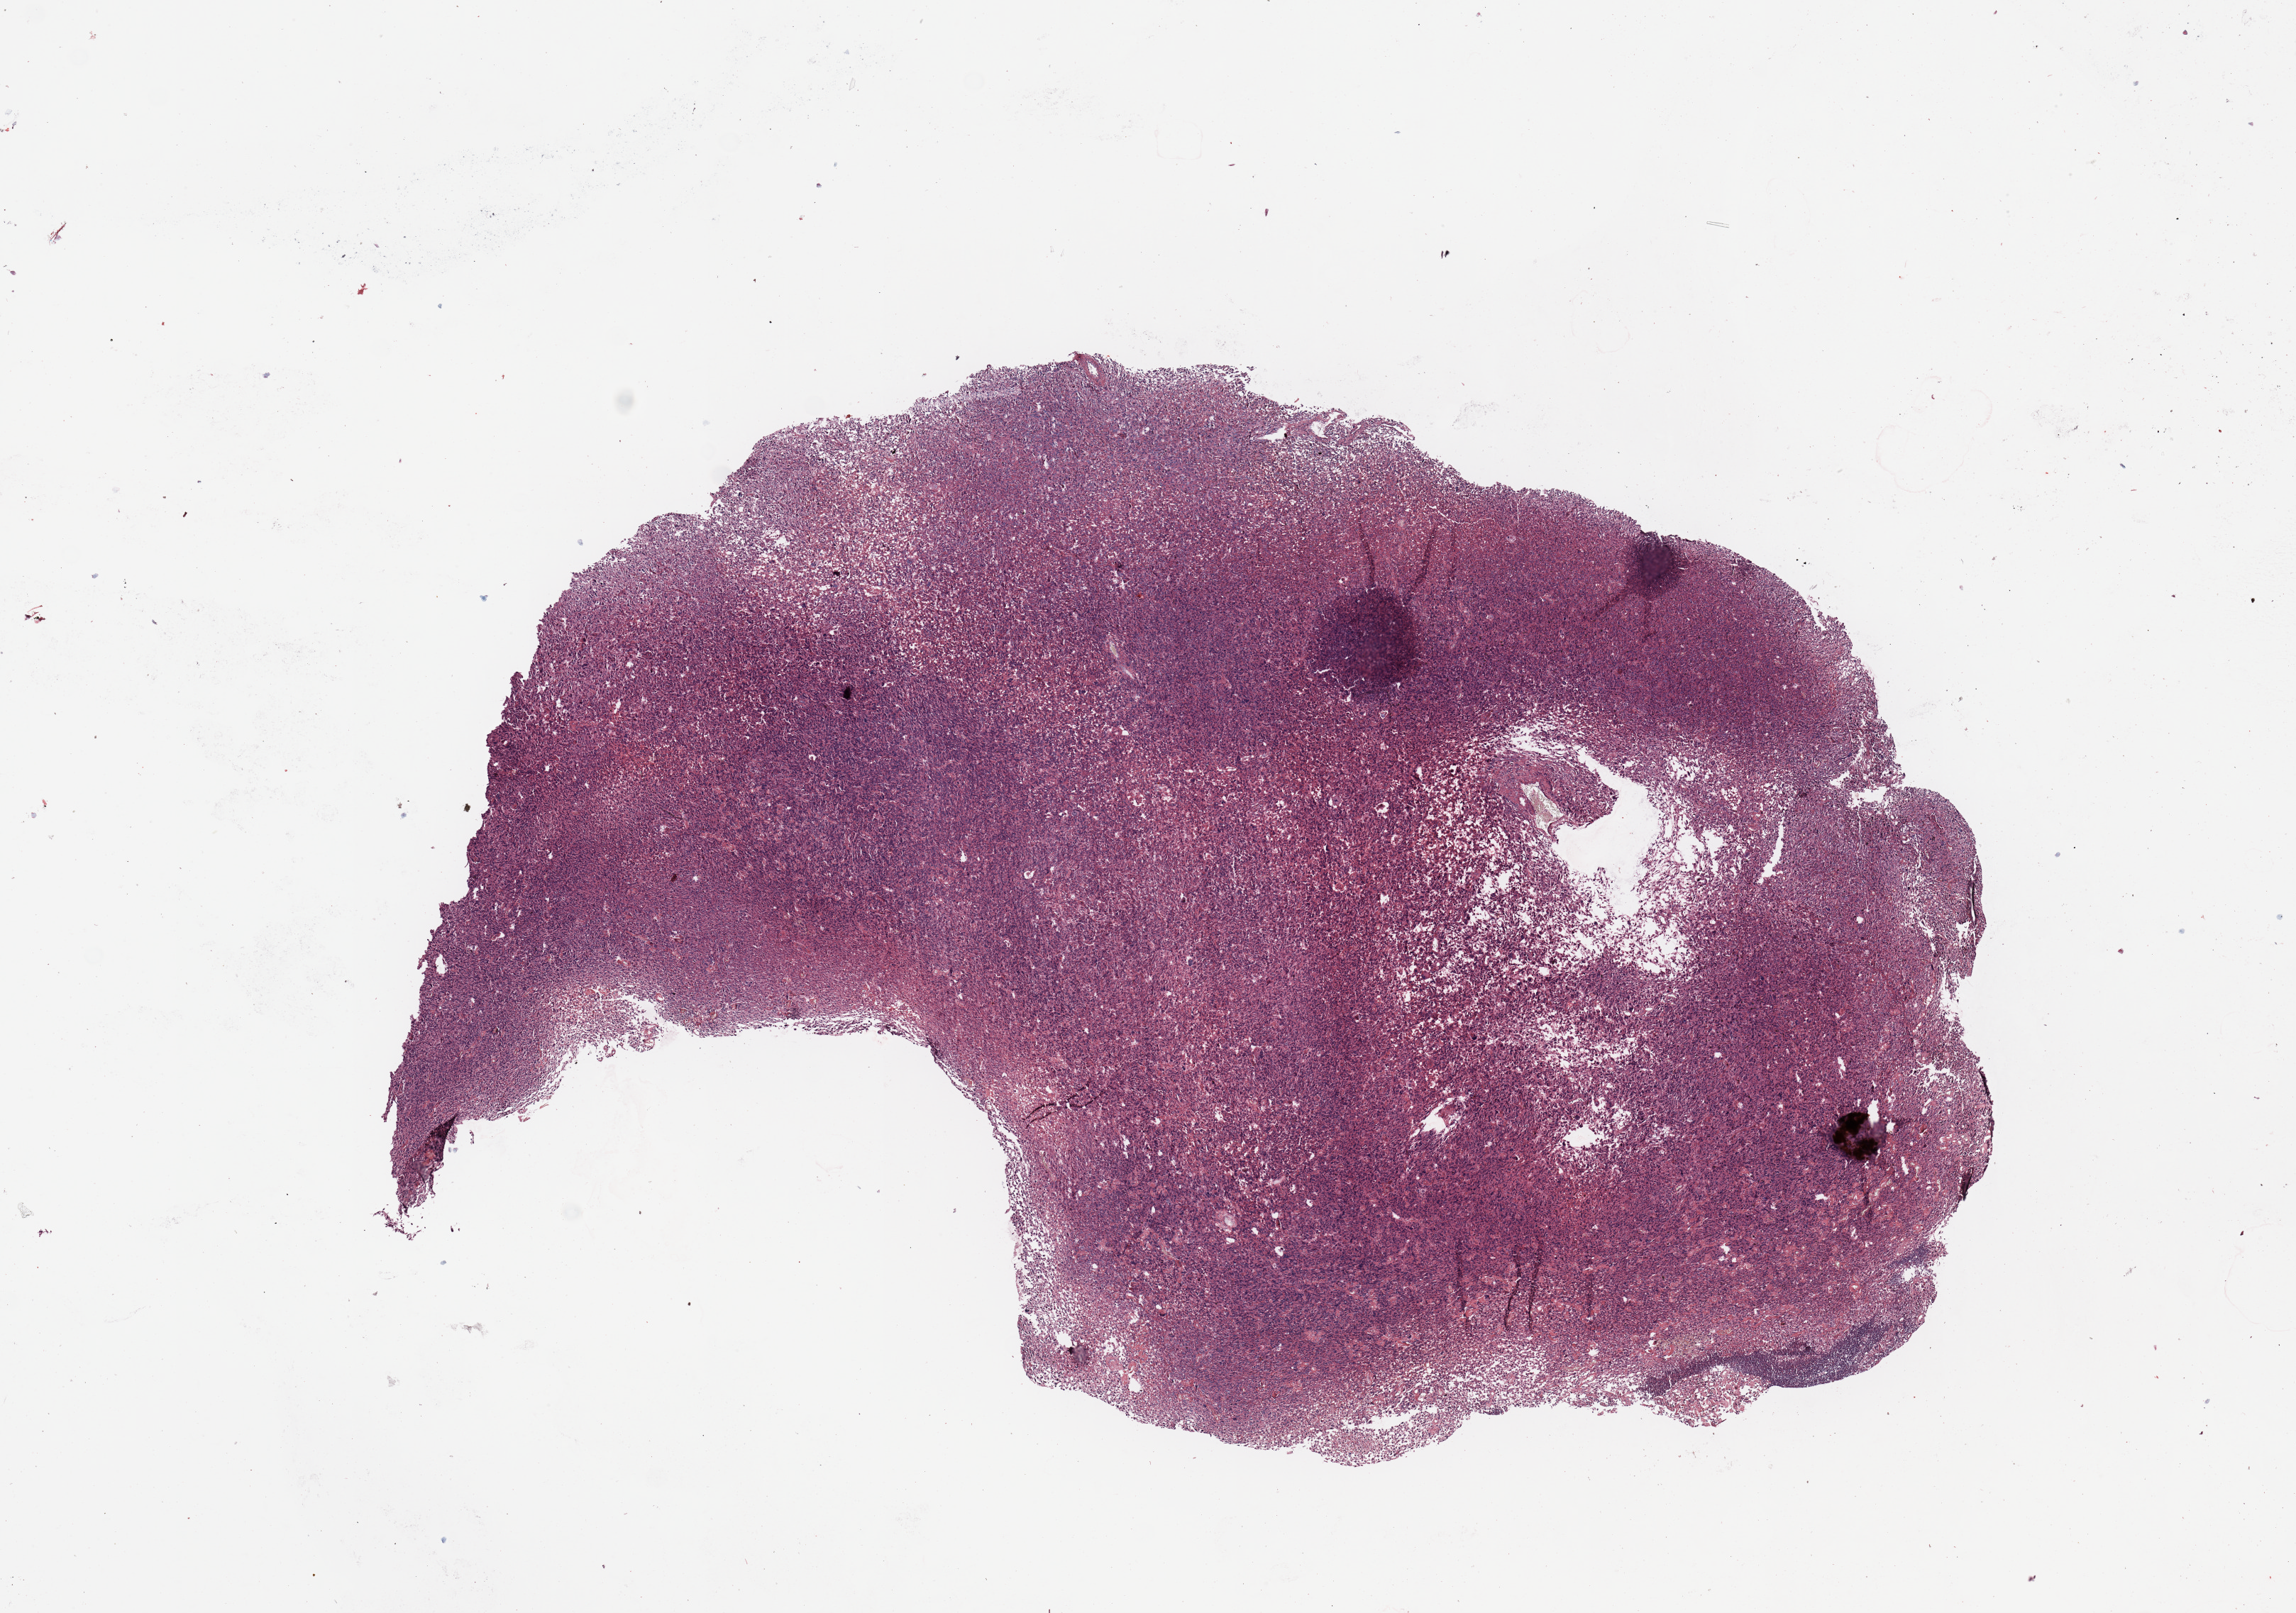
Whole-slide histology image, H&E-stained — shown as a low-resolution overview of the whole scanned area (about 12.8 x 9.0 mm, acquisition: 20x scan), tumour tissue sample. Patient: female, age 58 years.
Patient diagnosis (cohort enrolment): sarcoma (site not recorded at cohort level). Primary tumour site (as recorded): upper extremity.